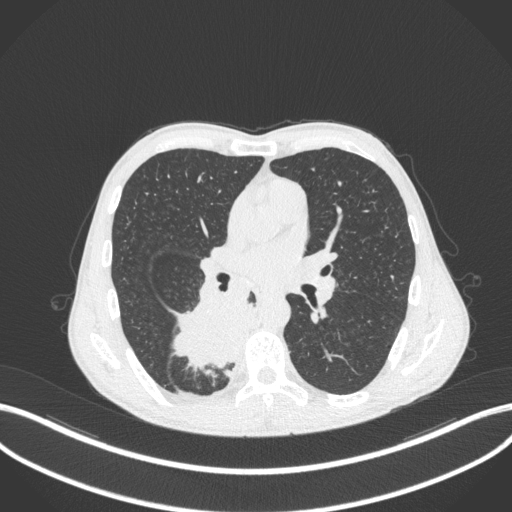
Chest CT, one axial slice. Slice 201 of 371 in the series (ordered by position). Reconstruction kernel B31f. Lung window (W 1500 / L -600 HU). 1 mm slice thickness. 512 × 512 image matrix. Male patient, age 58 years. Case-level facts recorded for this patient, not image findings: clinical TNM (as recorded): T3 N1 M1.
Outlined on this slice (bounding box drawn by a radiologist):
- lung tumour (recorded histology: squamous cell carcinoma): bounding box [x1, y1, x2, y2] px = [168, 294, 251, 371]